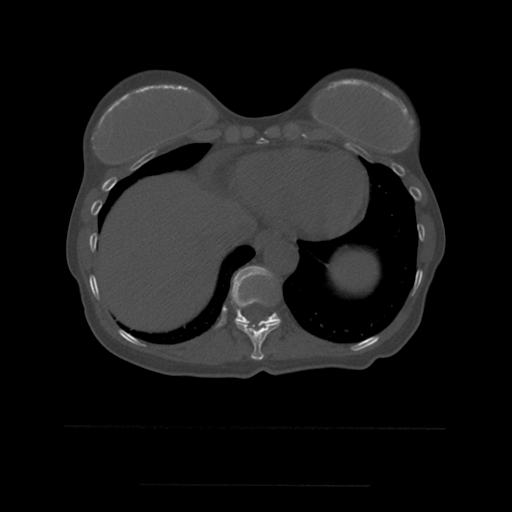
CT including the spine, one axial slice; position 292 of 544 along the scan axis; bone window (W 1800 / L 400 HU); 1.25 mm slice thickness; 512 × 512 image matrix, field of view 350 × 350 mm. Patient age 58 years. Case-level facts recorded for this patient, not image findings: primary cancer: lung.
Annotated regions visible in this slice (semi-automatic segmentation, software-assisted and operator-edited):
- T10 vertebra: box from (x=236, y=321) to (x=281, y=360) px
- T11 vertebra: (x=221, y=266)–(x=281, y=324)